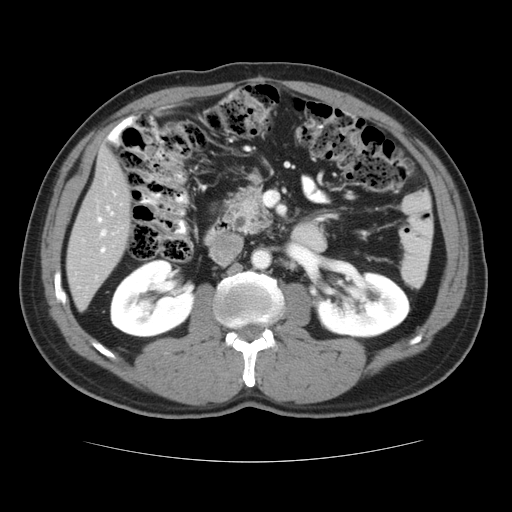
Contrast-enhanced abdominal CT, one axial slice; 120 kVp; intravenous contrast given; soft-tissue window (W 400 / L 40 HU); 5 mm slice thickness; 512 × 512 image matrix, field of view 374 × 374 mm. Male patient, age 66 years. From the clinical record (not read from this slice): diagnosis: colorectal cancer liver metastases, imaged before liver resection; multiple liver metastases: yes; largest metastasis: 1.6 cm; disease in both lobes: yes.
Structures marked on this image (outlined manually by an expert reader):
- hepatic veins: bounding box <99,205,114,238> (left, top, right, bottom; pixels)
- liver: <68,147,133,310>
- planned liver remnant (the part of the liver to remain after resection): <68,183,131,310>
- portal vein (with intrahepatic branches): <98,218,105,252>